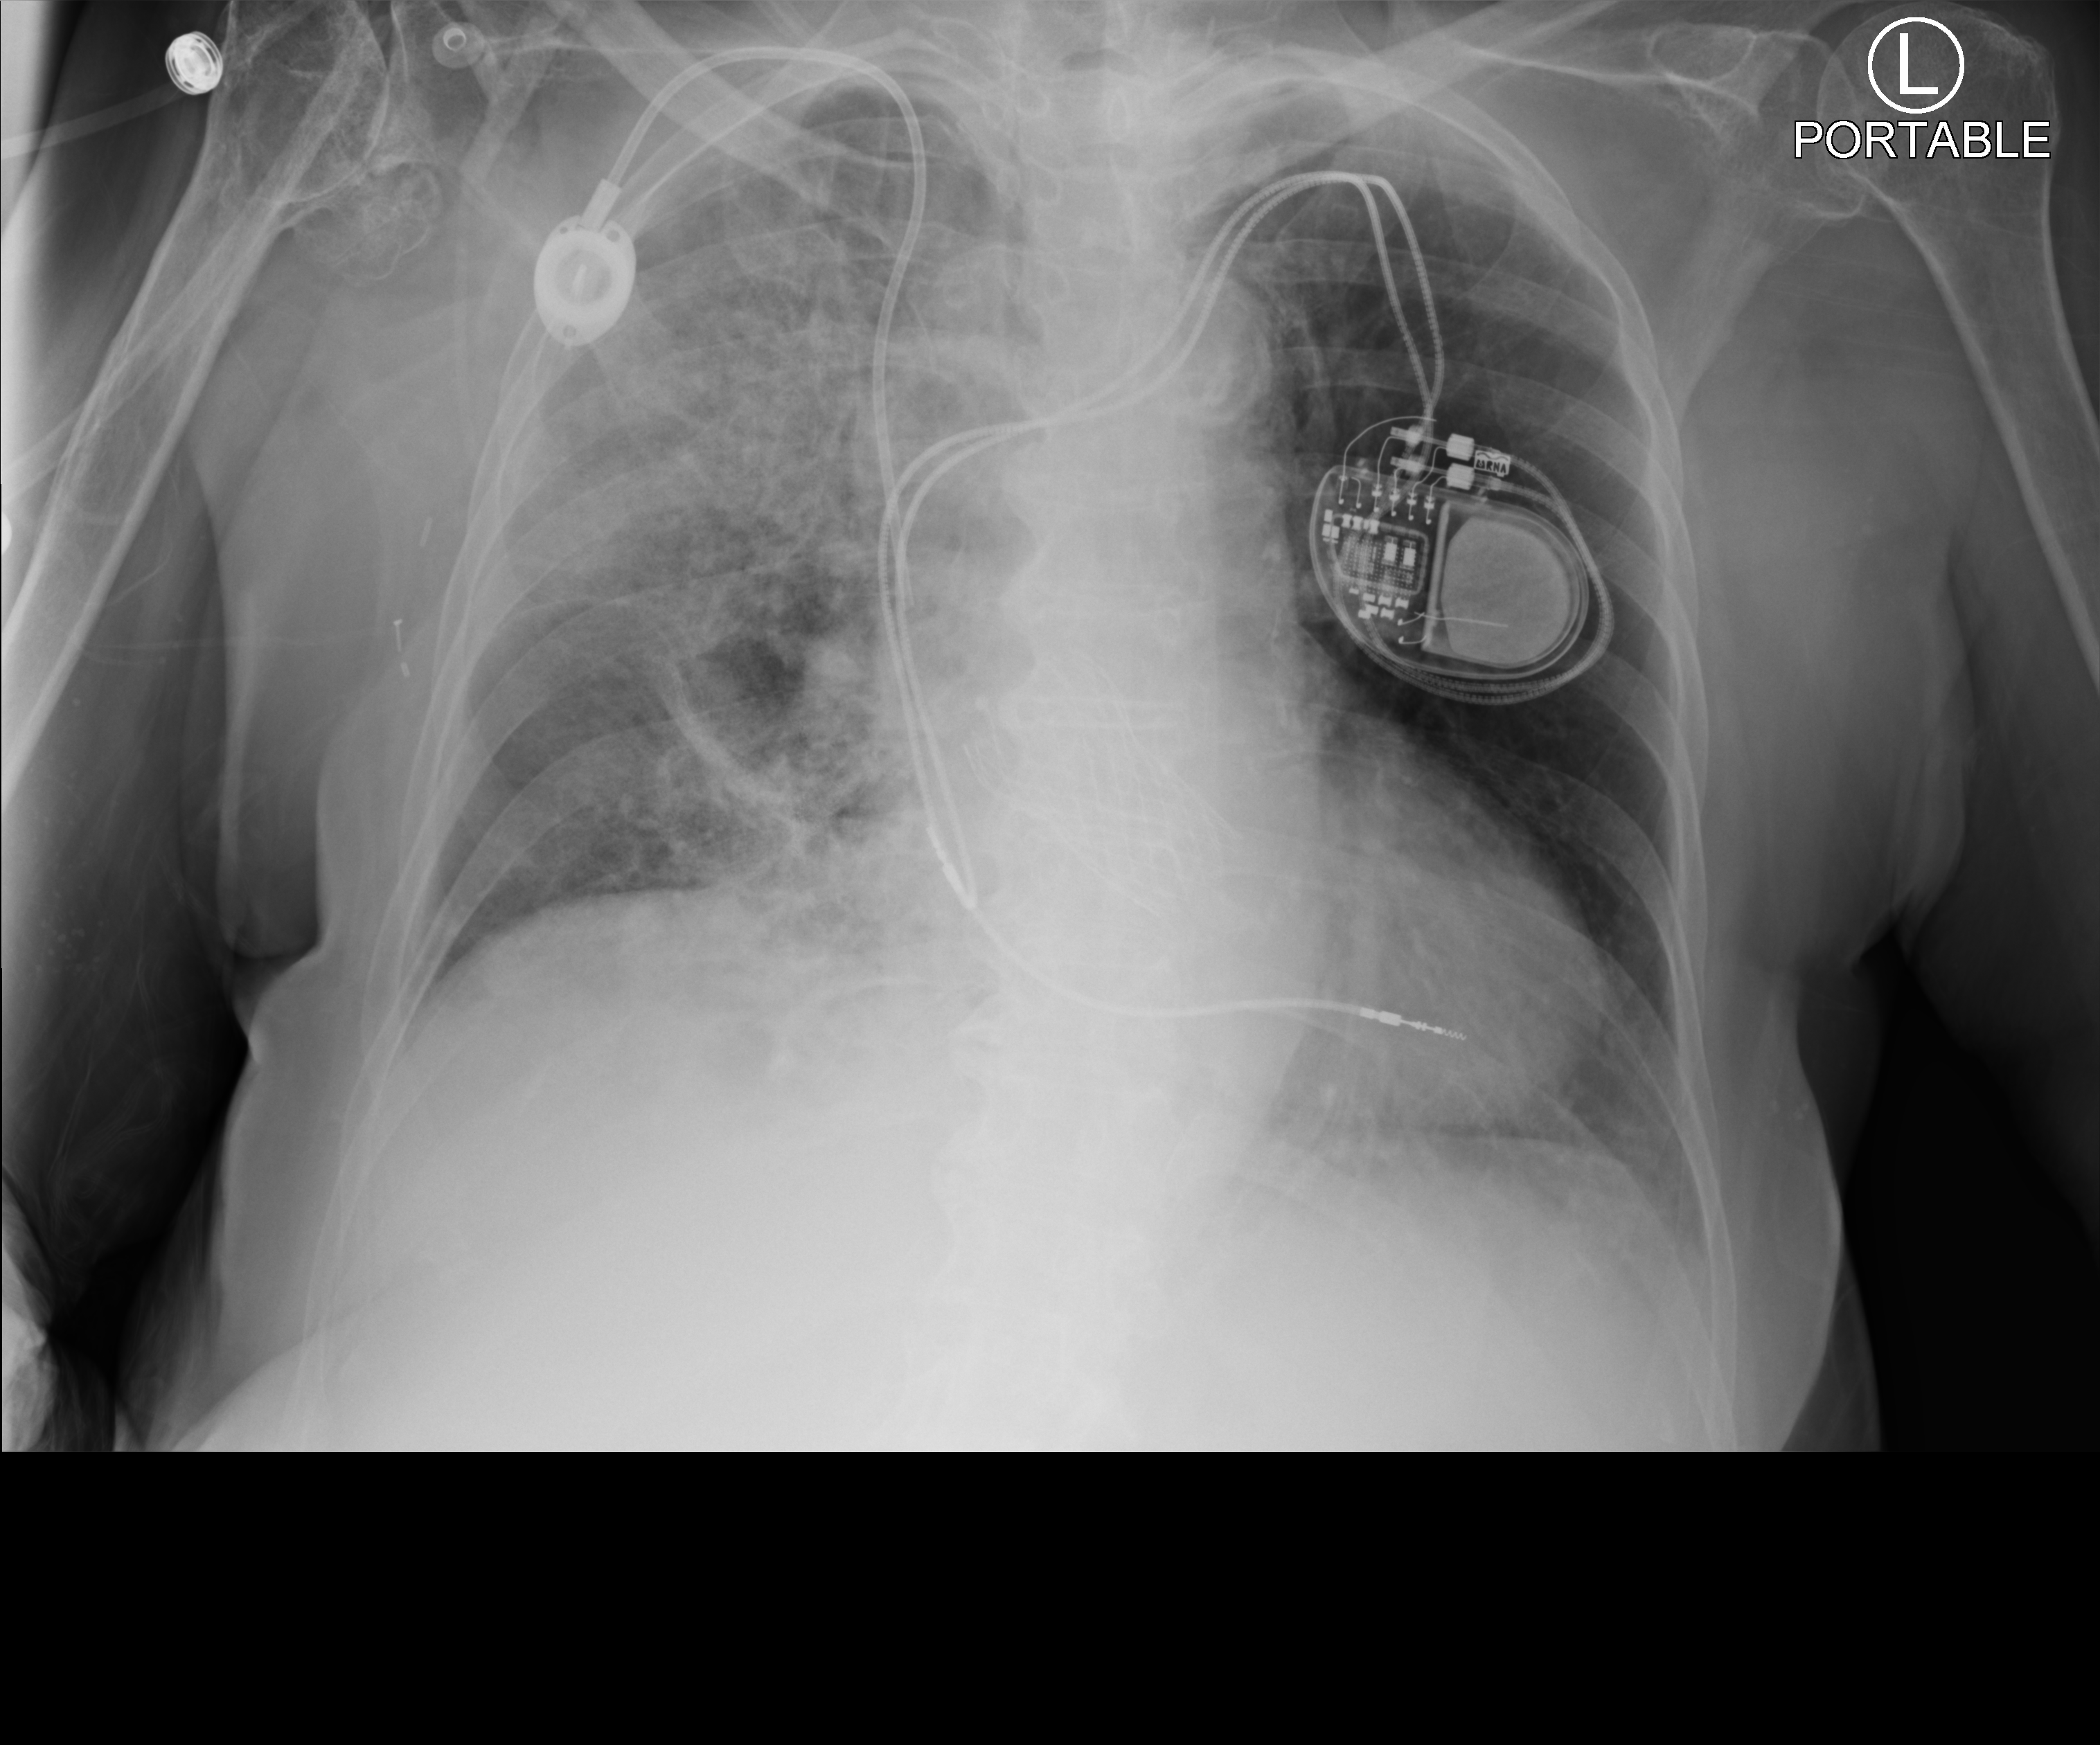
Portable chest radiograph, anteroposterior (AP) projection. Female patient hospitalised with COVID-19, age 75–90 years.
Hospital-stay facts (about this admission, not read from this image; timing relative to this image not recorded):
- admitted to intensive care during this hospital stay: no
- mechanically ventilated during this hospital stay: no